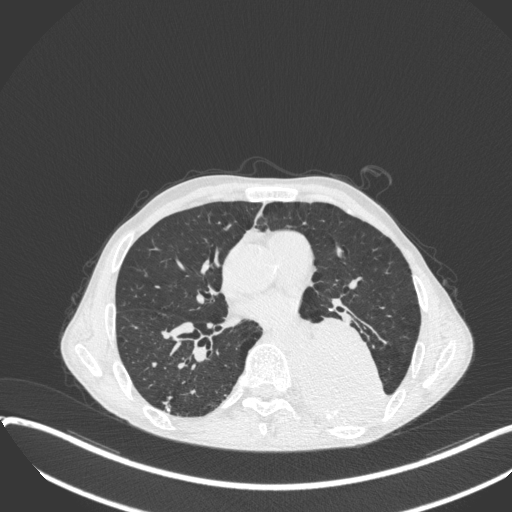
Chest CT, one axial slice. Position 183 of 400 along the scan axis. Reconstruction kernel B31f. 120 kVp. Lung window (W 1500 / L -600 HU). 1 mm slice thickness. 512 × 512 image matrix. Patient: male, 57 years. Case-level facts recorded for this patient, not image findings: clinical TNM (as recorded): T4 N0 M0.
Outlined on this slice (rectangle marked by the reading radiologist):
- lung tumour (recorded histology: squamous cell carcinoma): bounding box [x1, y1, x2, y2] px = [292, 316, 388, 421]